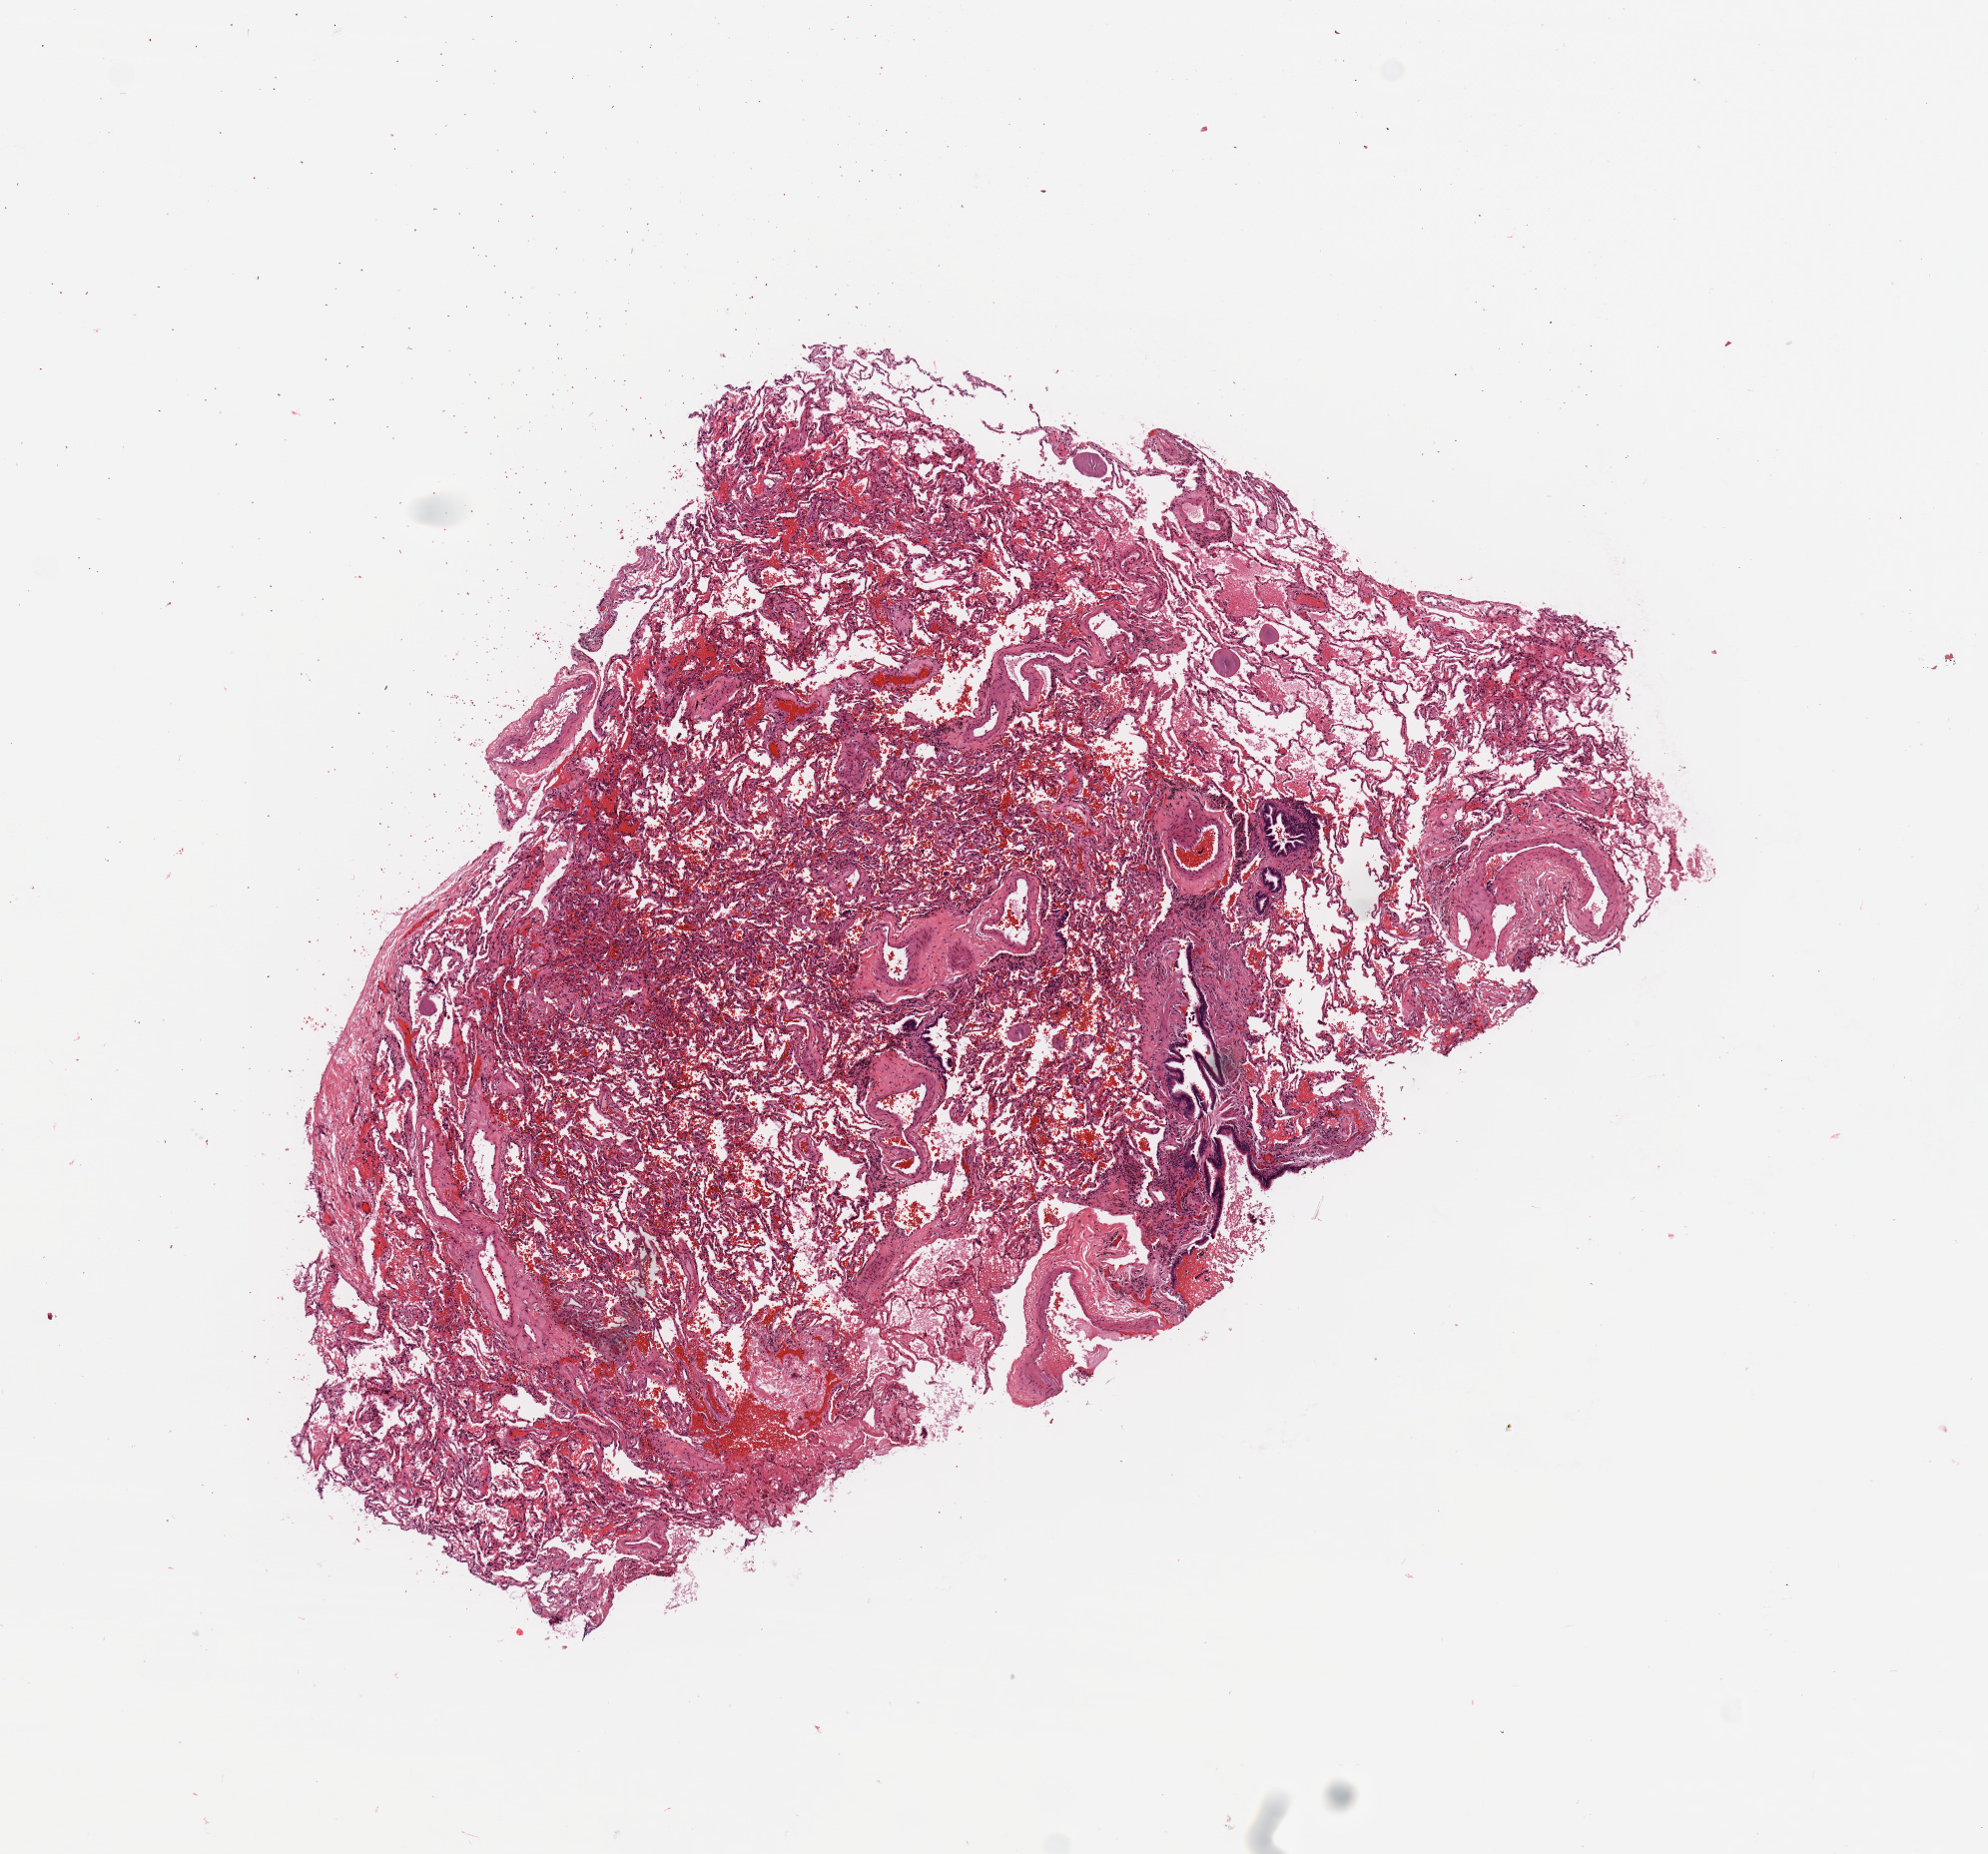
Digitized H&E tissue section (whole slide), a low-resolution overview of the entire scanned area, about 7.9 x 7.3 mm (acquisition: 20x scan). Normal (non-tumour) tissue sample, lung. Patient: male, age 65 years.
This section: normal (non-tumour) tissue from the same patient. Patient diagnosis: Adenocarcinoma, NOS.